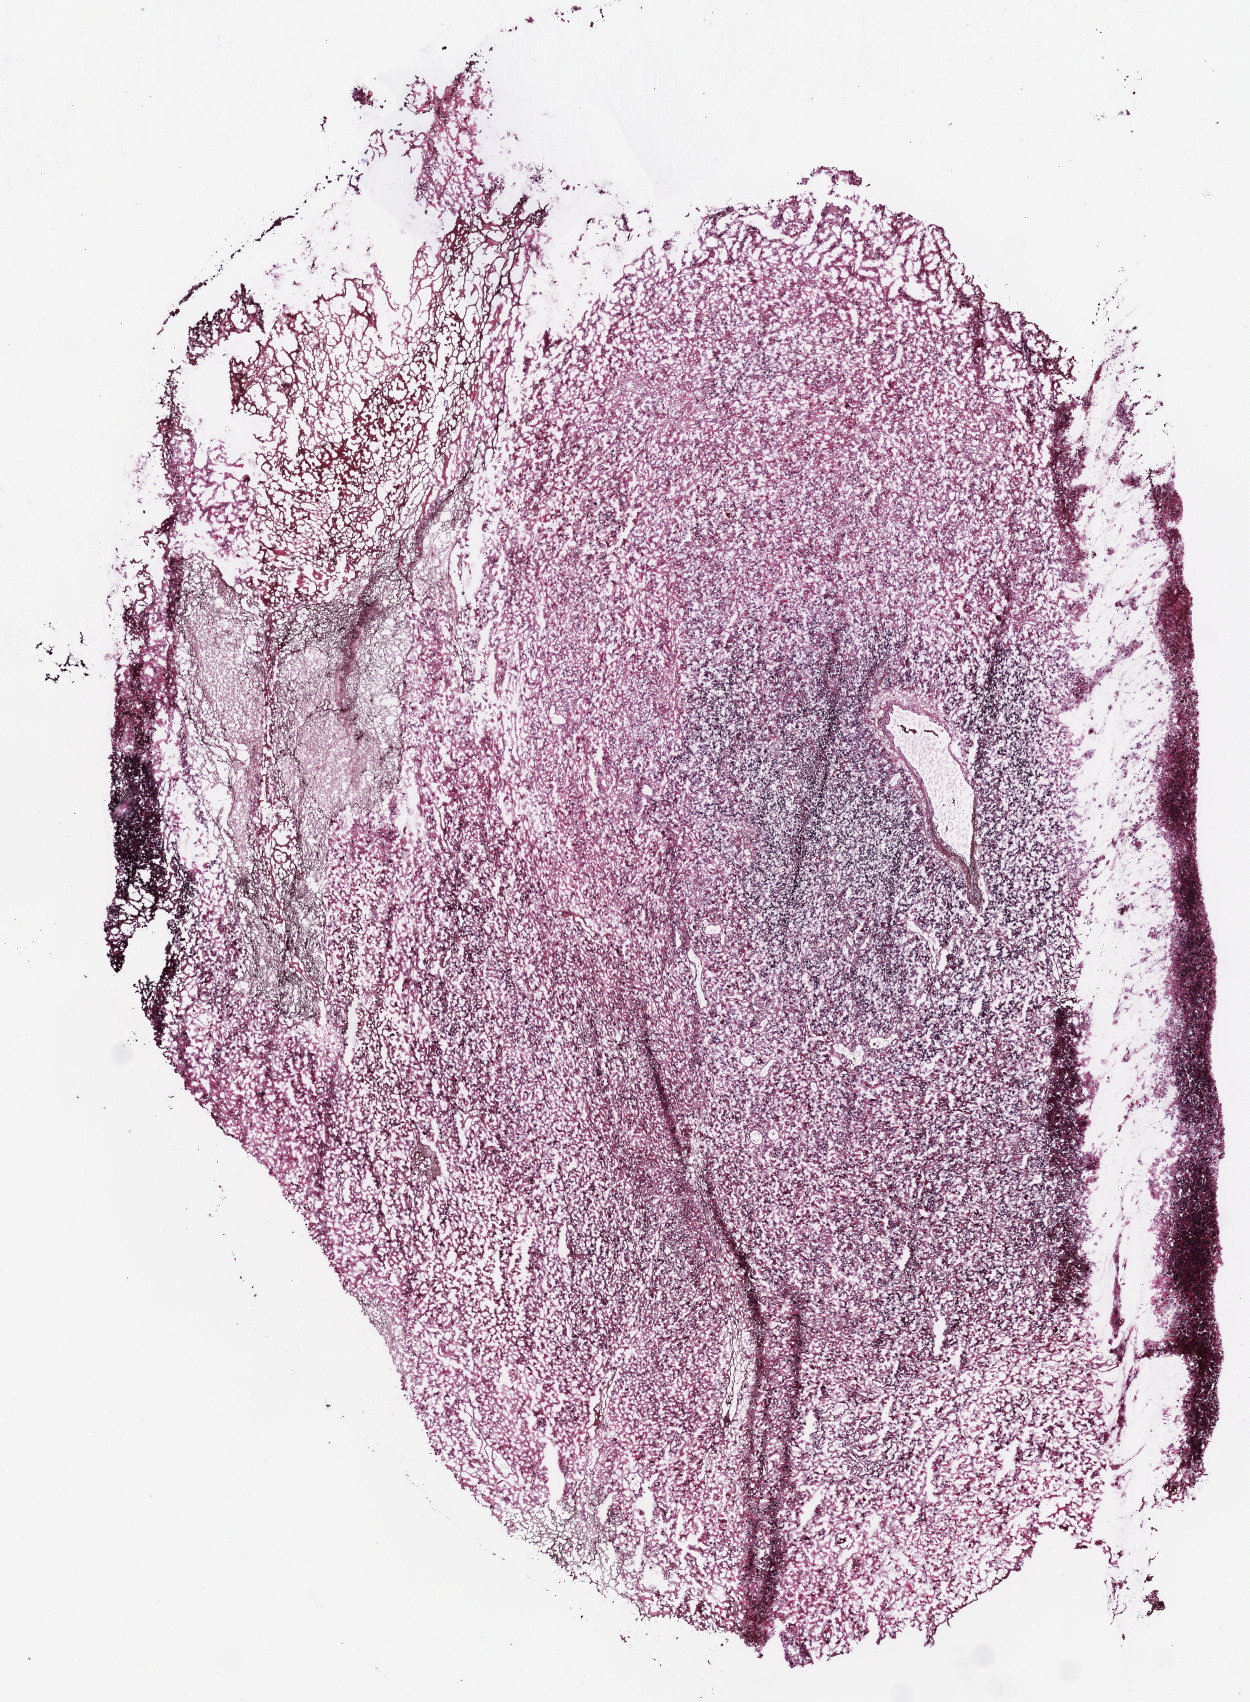
Whole-slide histology image, H&E — shown as a low-resolution overview of the whole scanned area (about 5.0 x 6.8 mm, acquisition: 20x scan), frozen section from the bottom of the tissue portion, primary tumour sample from the brain. Male, age 25 years at initial diagnosis. Composition of this section per pathologist review: tumour cells 100%, tumour nuclei 85%, normal cells 0%, stromal cells 0%, necrosis 0%.
- histologic diagnosis: Glioblastoma